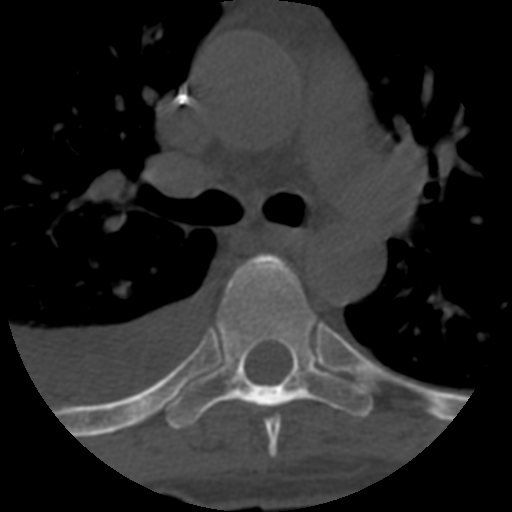
CT including the spine, one axial slice. Reconstruction kernel STANDARD. 120 kVp. One of 3 acquisitions stored at this slice position. Bone window (W 1800 / L 400 HU). 1.25 mm slice thickness. 512 × 512 image matrix. Patient age 55 years. From the clinical record (not read from this slice): primary cancer: colon.
Structures marked on this image (semi-automatic segmentation, software-assisted and operator-edited):
- T5 vertebra: bounding box [x1, y1, x2, y2] px = [265, 417, 281, 458]
- T6 vertebra: [166, 255, 373, 430]